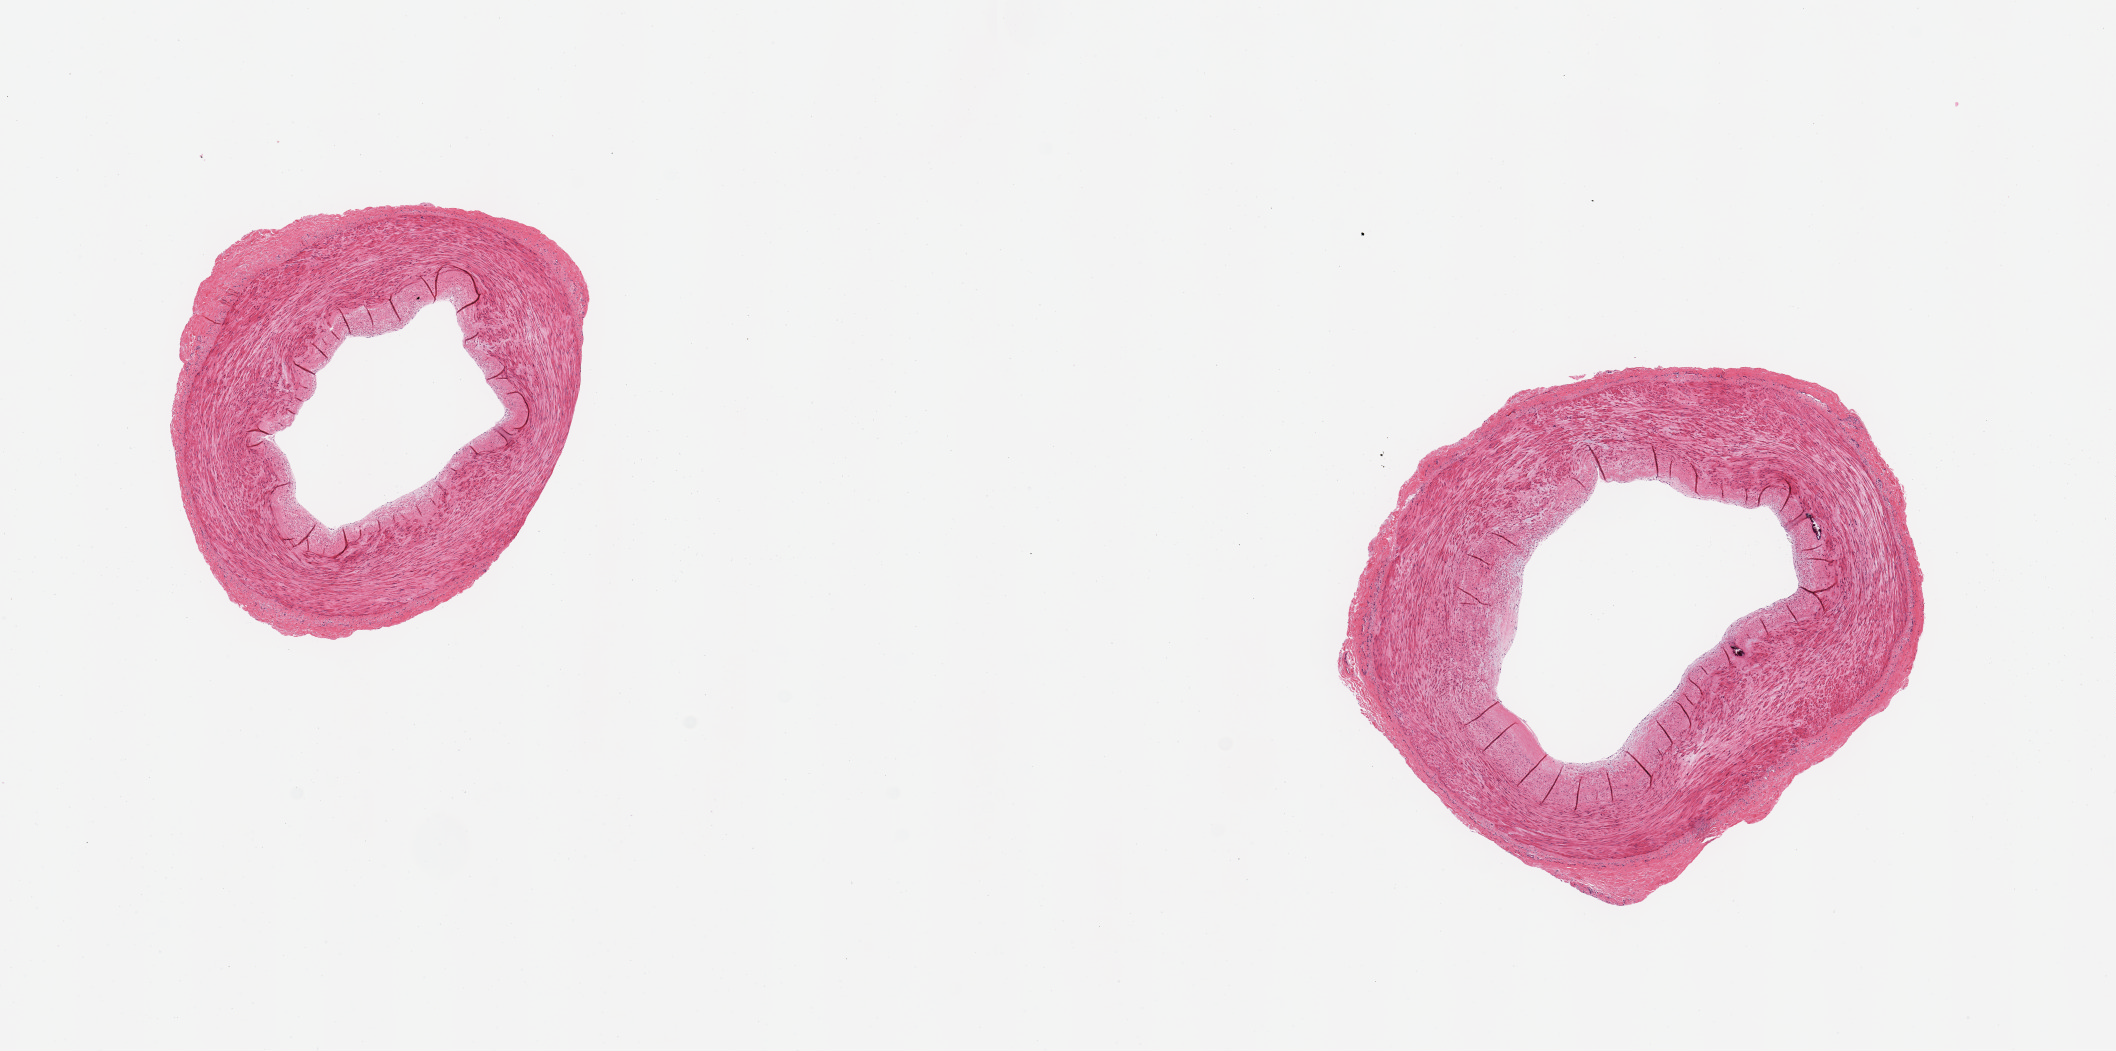
Whole-slide image, H&E stain, low-resolution overview of the scanned area, about 16.7 x 8.3 mm; PAXgene-fixed, paraffin-embedded tissue; target tissue: tibial artery; donor tissue sample. Donor sex: male.
Reviewer comment on this tissue sample: 2 pieces, no atherosis, minute foci of Monckeberg medial sclerosis.